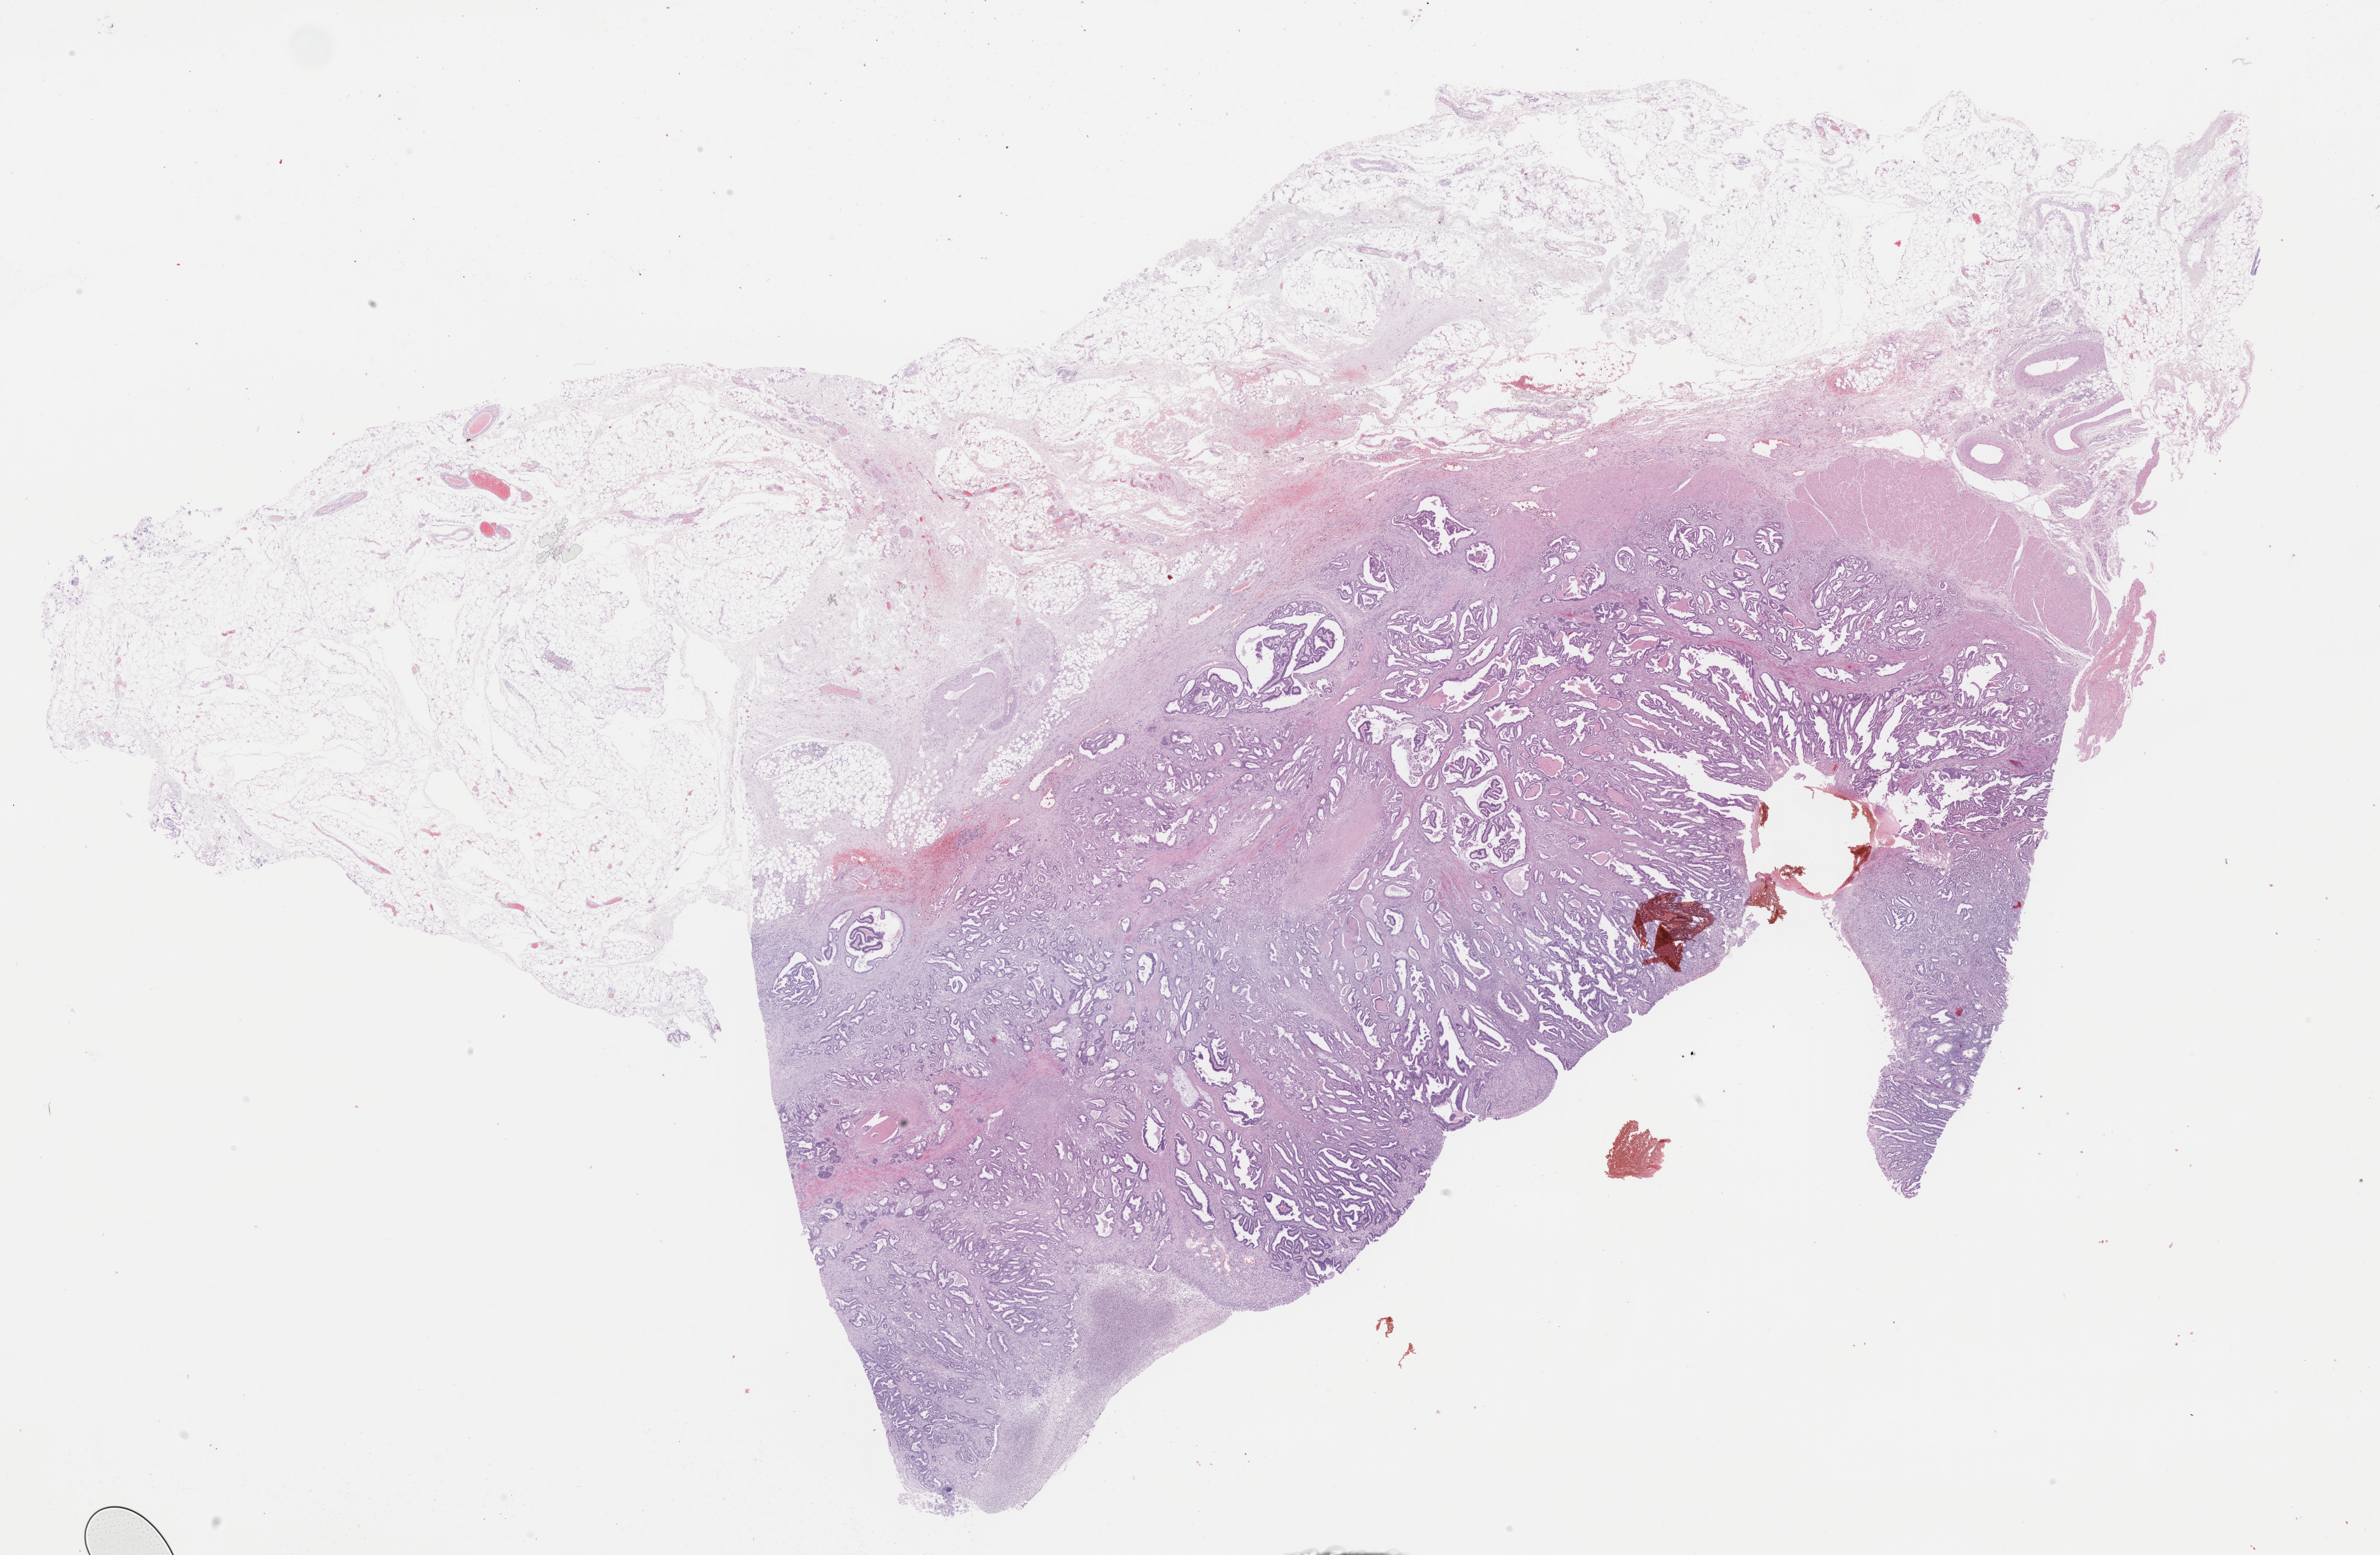
Digitized H&E-stained tissue section (whole slide), a low-resolution overview of the entire scanned area, about 31.2 x 20.4 mm (from a 40x scan); formalin-fixed paraffin-embedded (FFPE) diagnostic section; stomach, primary tumour sample. Male, age 56 years at initial diagnosis. Histologic grade: G2 (moderately differentiated).
- histologic diagnosis: Tubular adenocarcinoma (cardia, NOS)
- AJCC pathologic stage: IIIA (7th edition)
- lymph nodes positive (case pathology): 14 of 14 examined